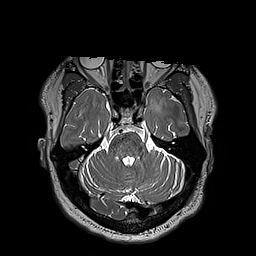
Brain MRI from a brain-tumour surgery series, one axial slice. Slice 133 of 192 in the series (ordered by position). 1 mm slice thickness. 256 × 256 image matrix. Case-level facts recorded for this patient, not image findings: histopathology: Astrocytoma; WHO grade: 3; IDH mutation: yes.
Annotated regions visible in this slice (expert manual segmentation):
- tumour: box from (x=150, y=98) to (x=165, y=112) px